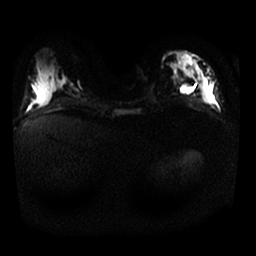
Breast MRI, one axial slice; diffusion-weighted series; image 2 of 4 stored at this slice position (different b-values; order by instance number); 1.5 T; 4 mm slice thickness; 256 × 256 image matrix, field of view 320 × 320 mm. Female patient.
Annotated regions visible in this slice (expert manual segmentation):
- tumour on diffusion-weighted imaging: bounding box <202,76,213,96> (left, top, right, bottom; pixels)